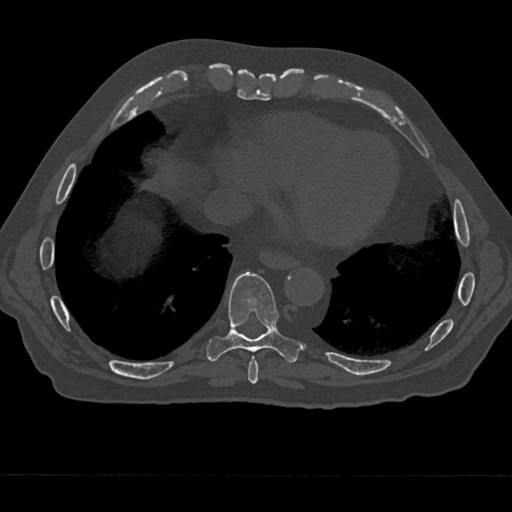
CT including the spine, one axial slice. Slice 266 of 797 in the series (ordered by position). Bone window (W 1800 / L 400 HU). 512 × 512 image matrix. Patient: male, 75 years. From the clinical record (not read from this slice): primary cancer: renal.
Outlined on this slice (semi-automatic segmentation, software-assisted and operator-edited):
- T8 vertebra: bounding box (x1, y1, x2, y2) in pixels: (248, 356, 259, 384)
- T9 vertebra: (207, 271, 302, 363)